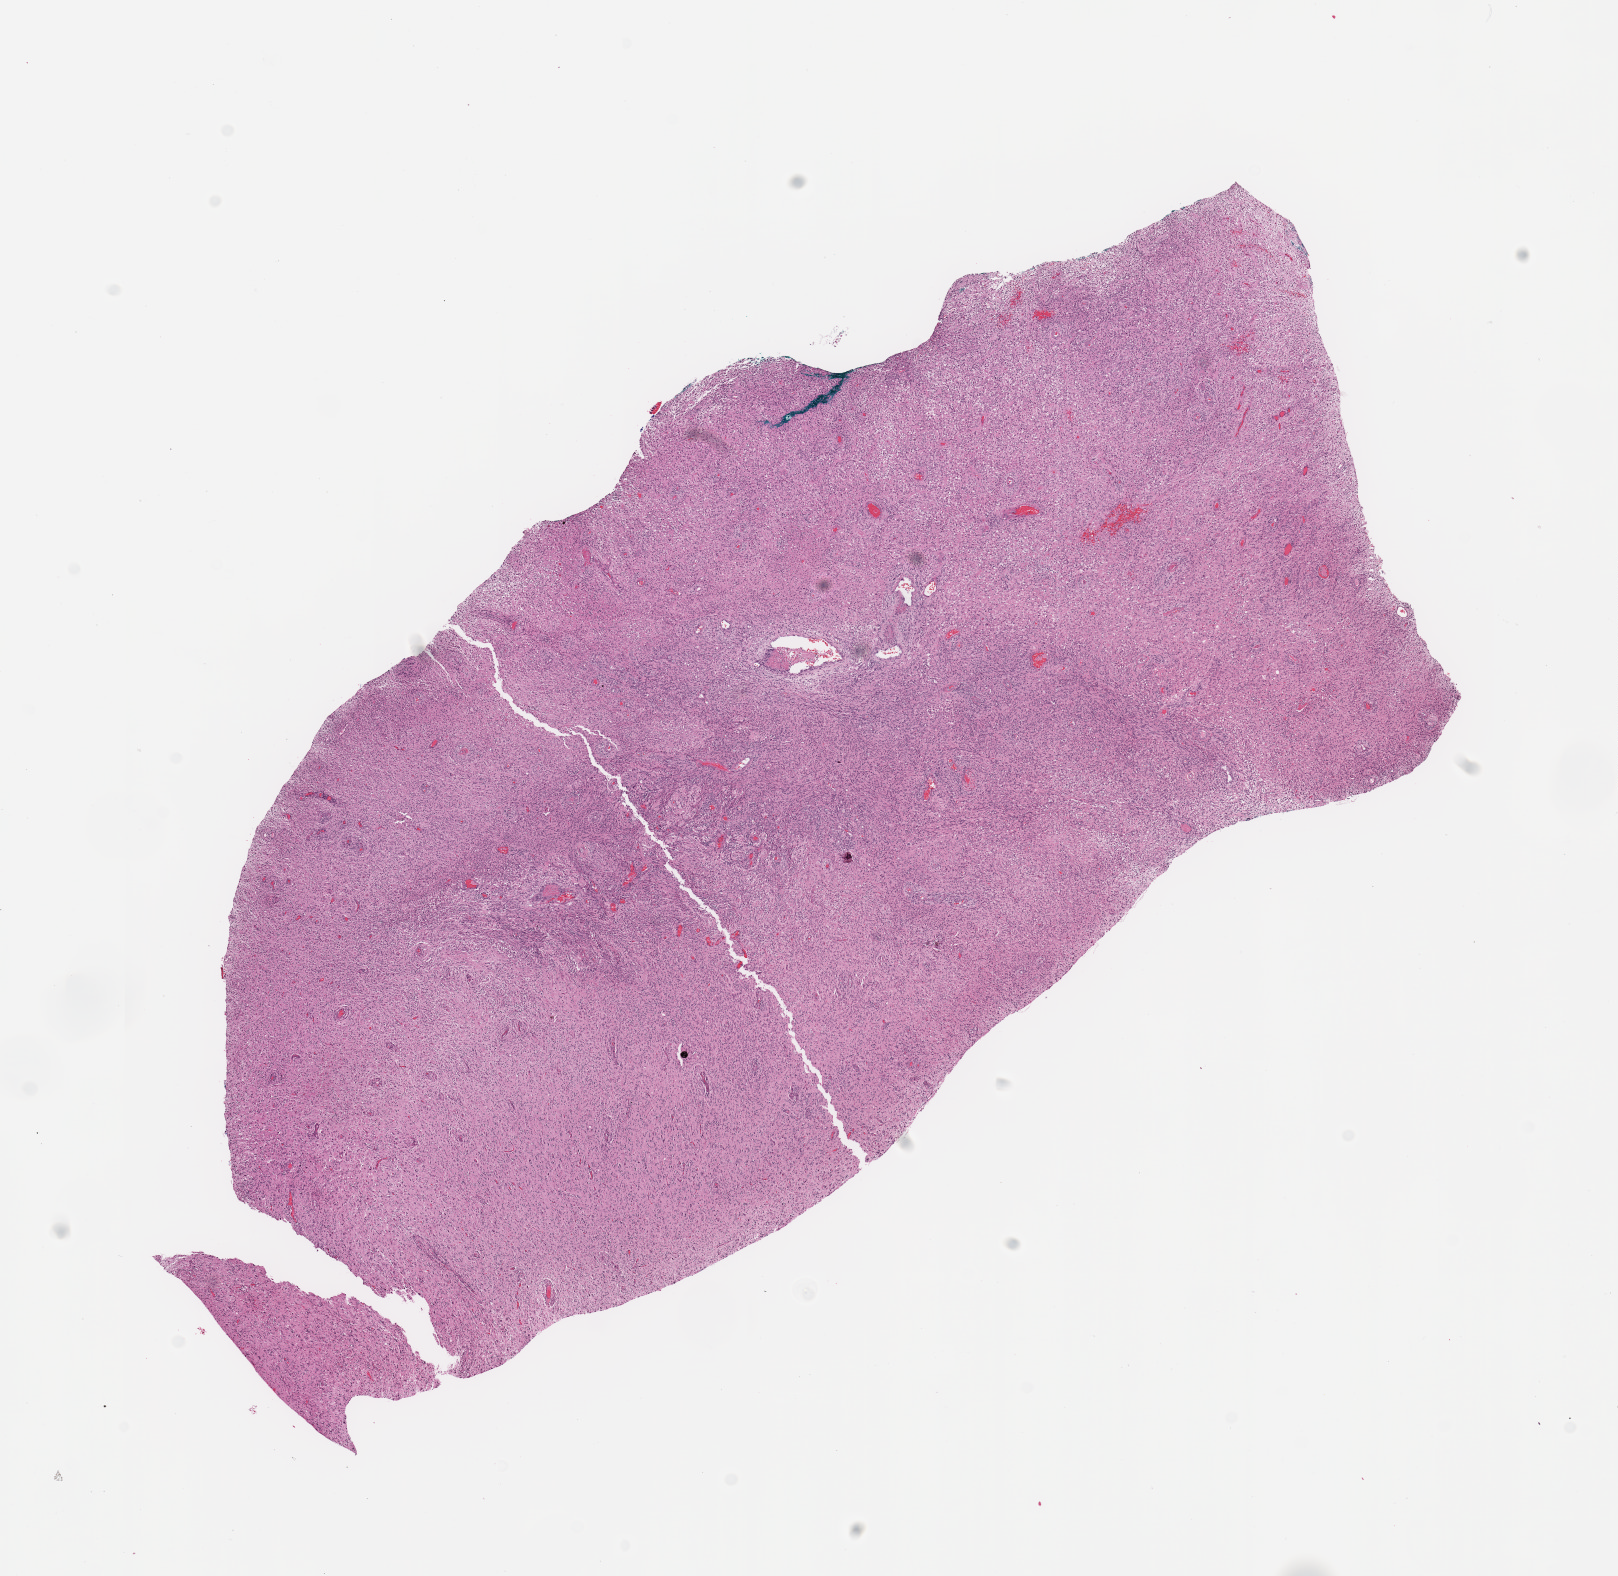
Digitized H&E-stained tissue section (whole slide), a low-resolution overview of the entire scanned area, about 12.8 x 12.5 mm, tumour tissue sample, sampled site: brain. Female, 66 y/o. Composition of this section per pathologist review: tumour nuclei 80%, necrosis 3%.
- histologic diagnosis: Glioblastoma